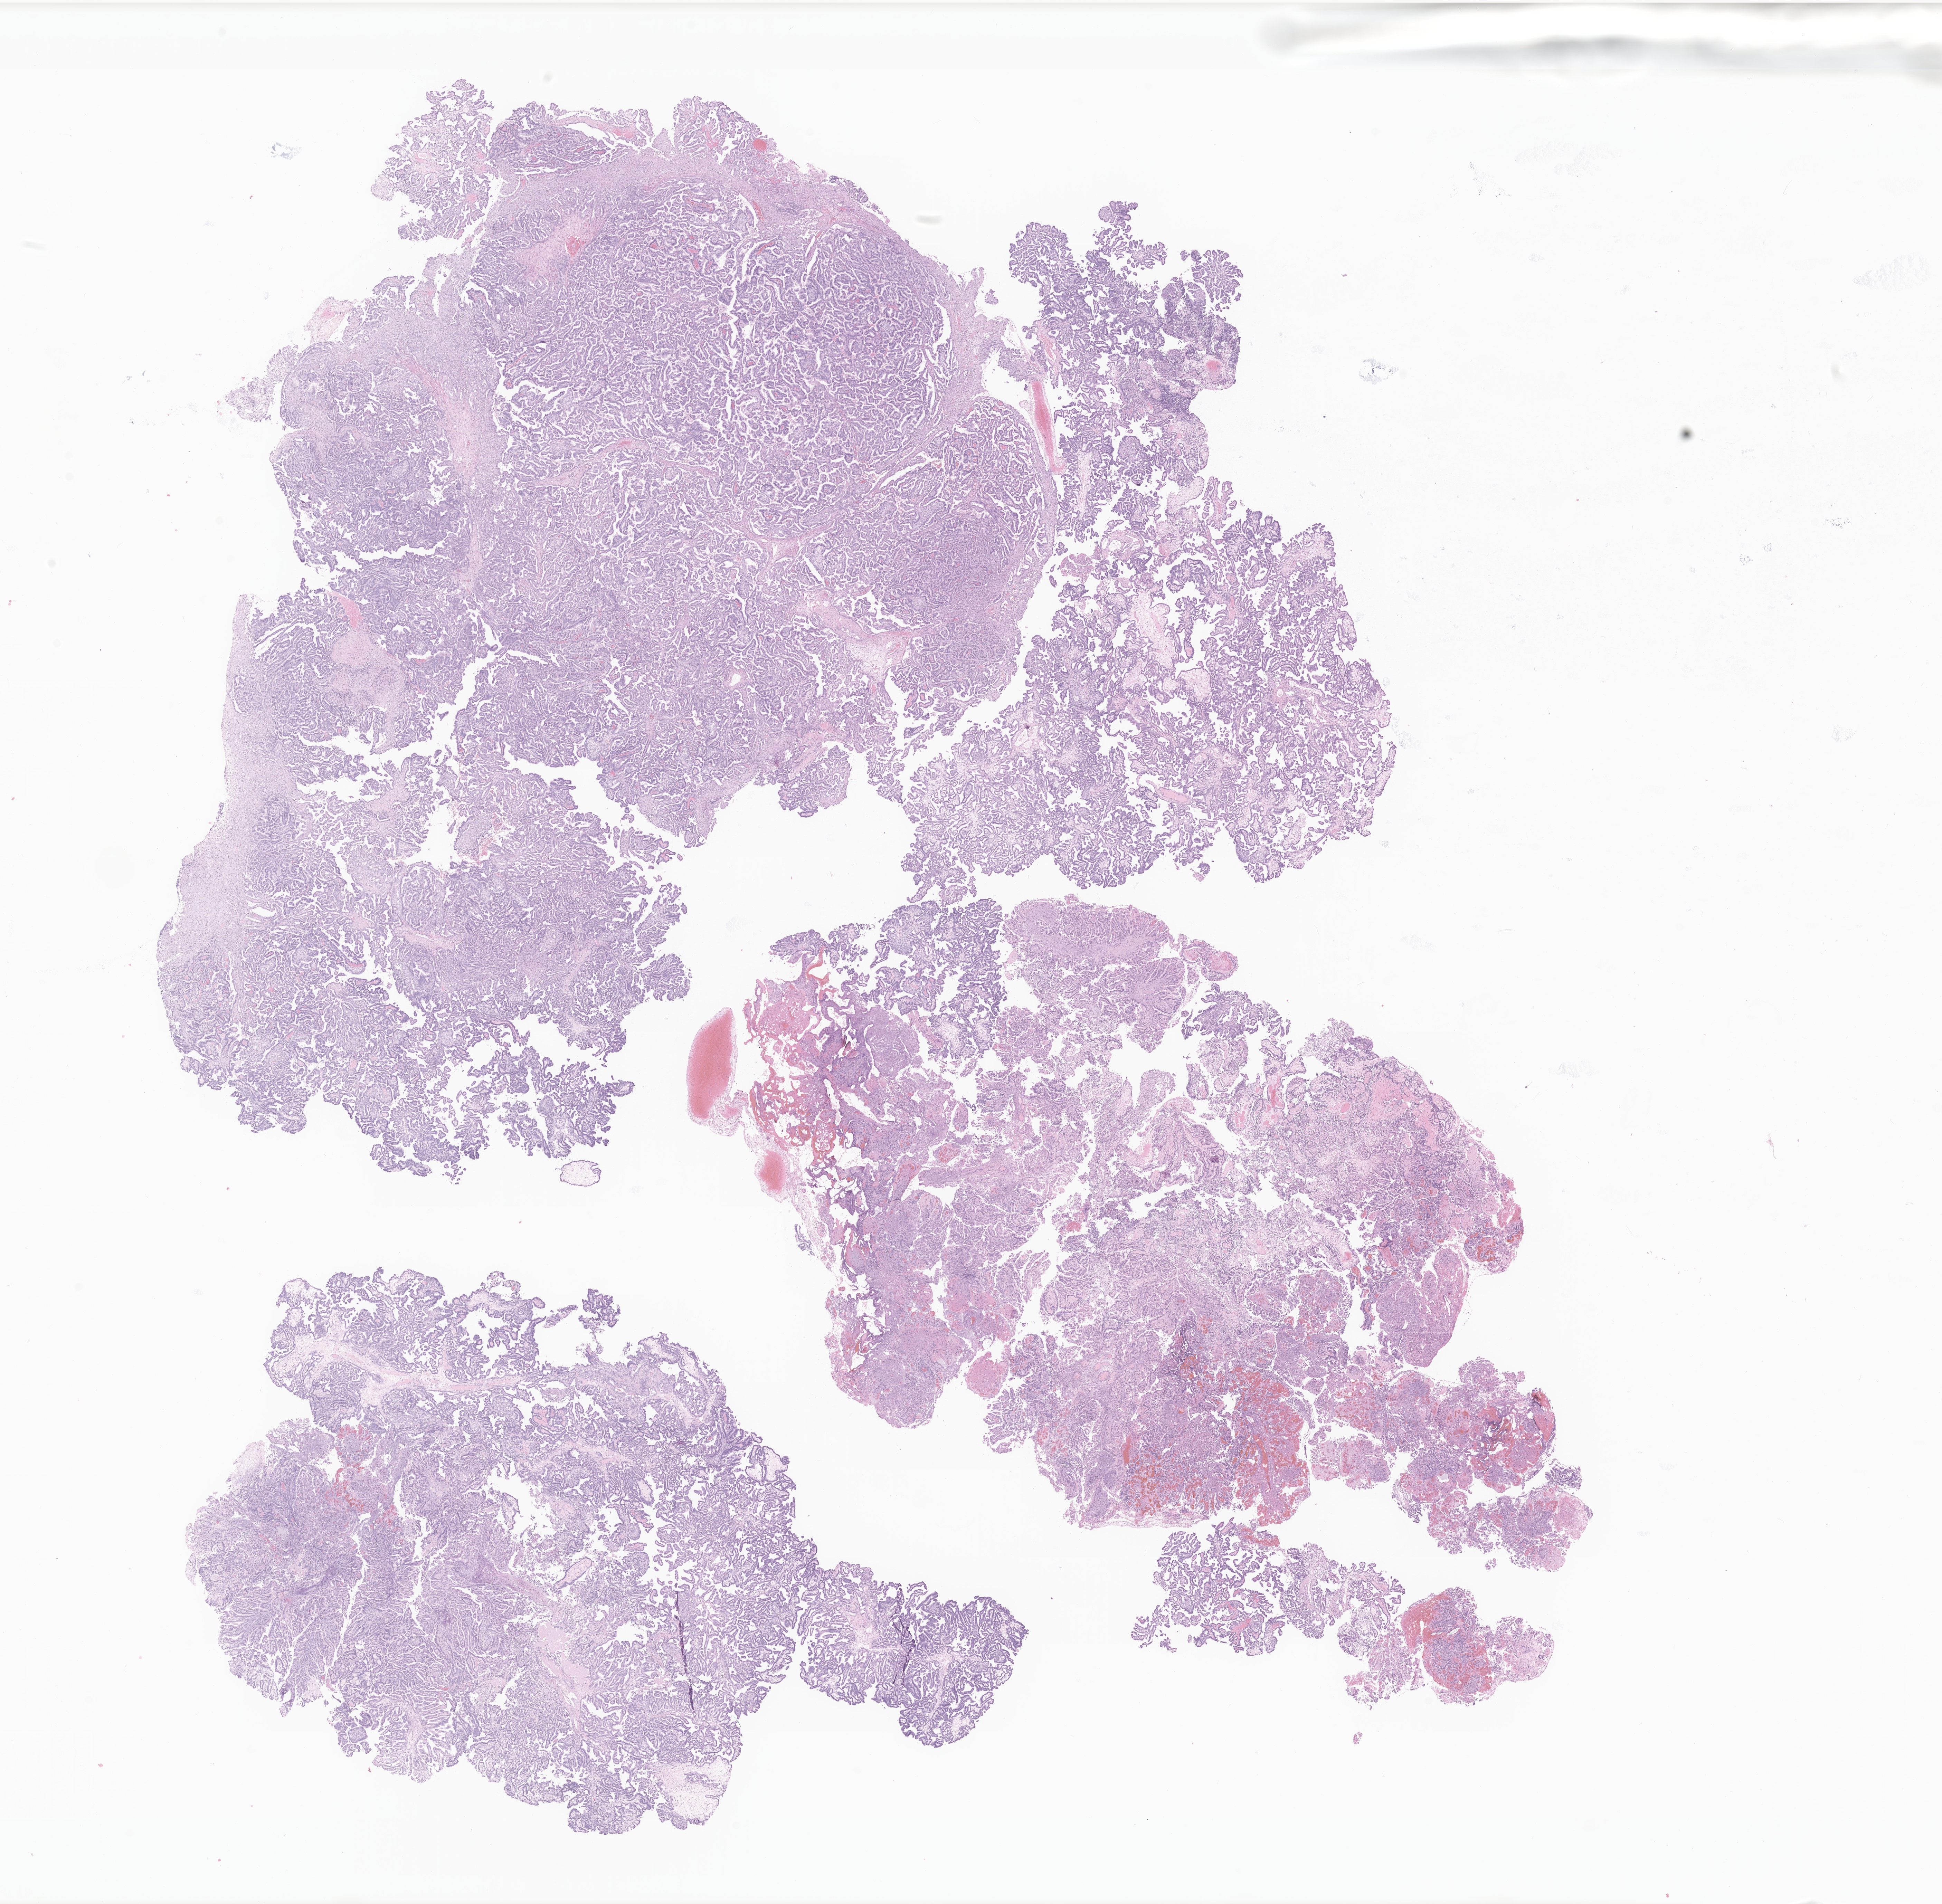
Digitized haematoxylin and eosin-stained section of tumor tissue from the cerebral ventricle, whole scanned area (about 23.7 x 23.2 mm) shown as a low-resolution overview, formalin-fixed paraffin-embedded section. Patient male; age 220 days.
Recorded diagnosis: Atypical choroid plexus papilloma.